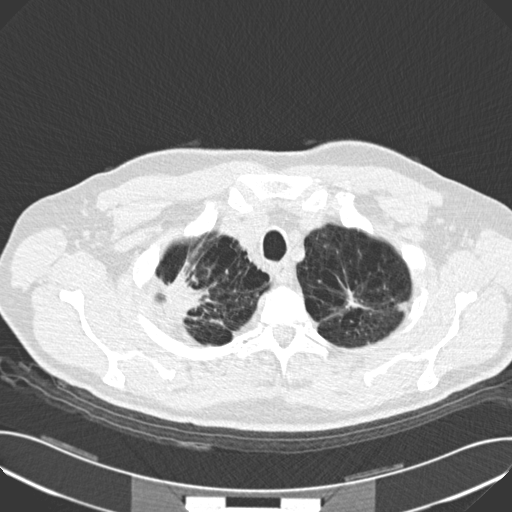
Low-dose screening chest CT, one axial slice; position 142 of 159 along the scan axis; reconstruction kernel B30f; 120 kVp; lung window (W 1500 / L -600 HU); 512 × 512 image matrix, field of view 380 × 380 mm.
Annotated regions visible in this slice (outlined manually by an expert reader):
- lesion 1 (tumor, upper lobe of right lung): bounding box (x1, y1, x2, y2) in pixels: (164, 277, 203, 321)